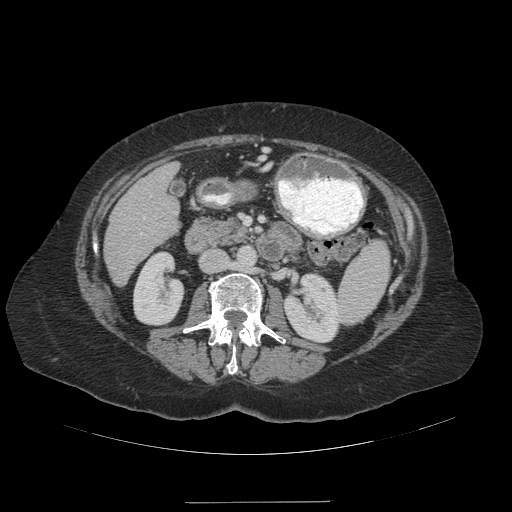
Contrast-enhanced abdominal CT (liver protocol), one axial slice; slice 45 of 99 in the series (ordered by position); reconstruction kernel STANDARD; 140 kVp; soft-tissue window (W 400 / L 40 HU); 2.5 mm slice thickness; 512 × 512 image matrix. From the clinical record (not read from this slice): diagnosis: hepatocellular carcinoma (patient treated with transarterial chemoembolisation; whether this scan precedes or follows treatment is not stated here); TNM stage (as recorded): Stage-IVA; Child-Pugh class: A; tumour nodularity: multinodular.
Annotated regions visible in this slice (semi-automatically segmented with operator editing):
- liver parenchyma outside the tumour (the mass and vessels are separate outlines, so this box may not span the whole liver): box from (x=104, y=164) to (x=178, y=286) px
- liver vessels: (x=141, y=217)–(x=145, y=234)